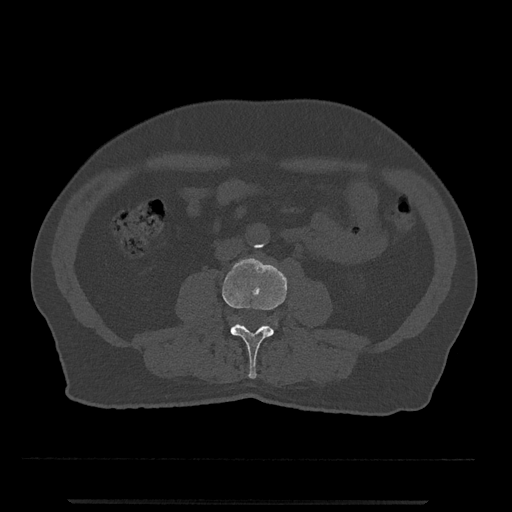
CT including the spine, one axial slice. Position 188 of 797 along the scan axis. 120 kVp. Bone window (W 1800 / L 400 HU). 512 × 512 image matrix. Patient: male, 63 years. Case-level facts recorded for this patient, not image findings: primary cancer: prostate.
Outlined on this slice (semi-automatic segmentation, software-assisted and operator-edited):
- L3 vertebra: box from (x=222, y=258) to (x=287, y=379) px
- L4 vertebra: (x=229, y=320)–(x=278, y=326)